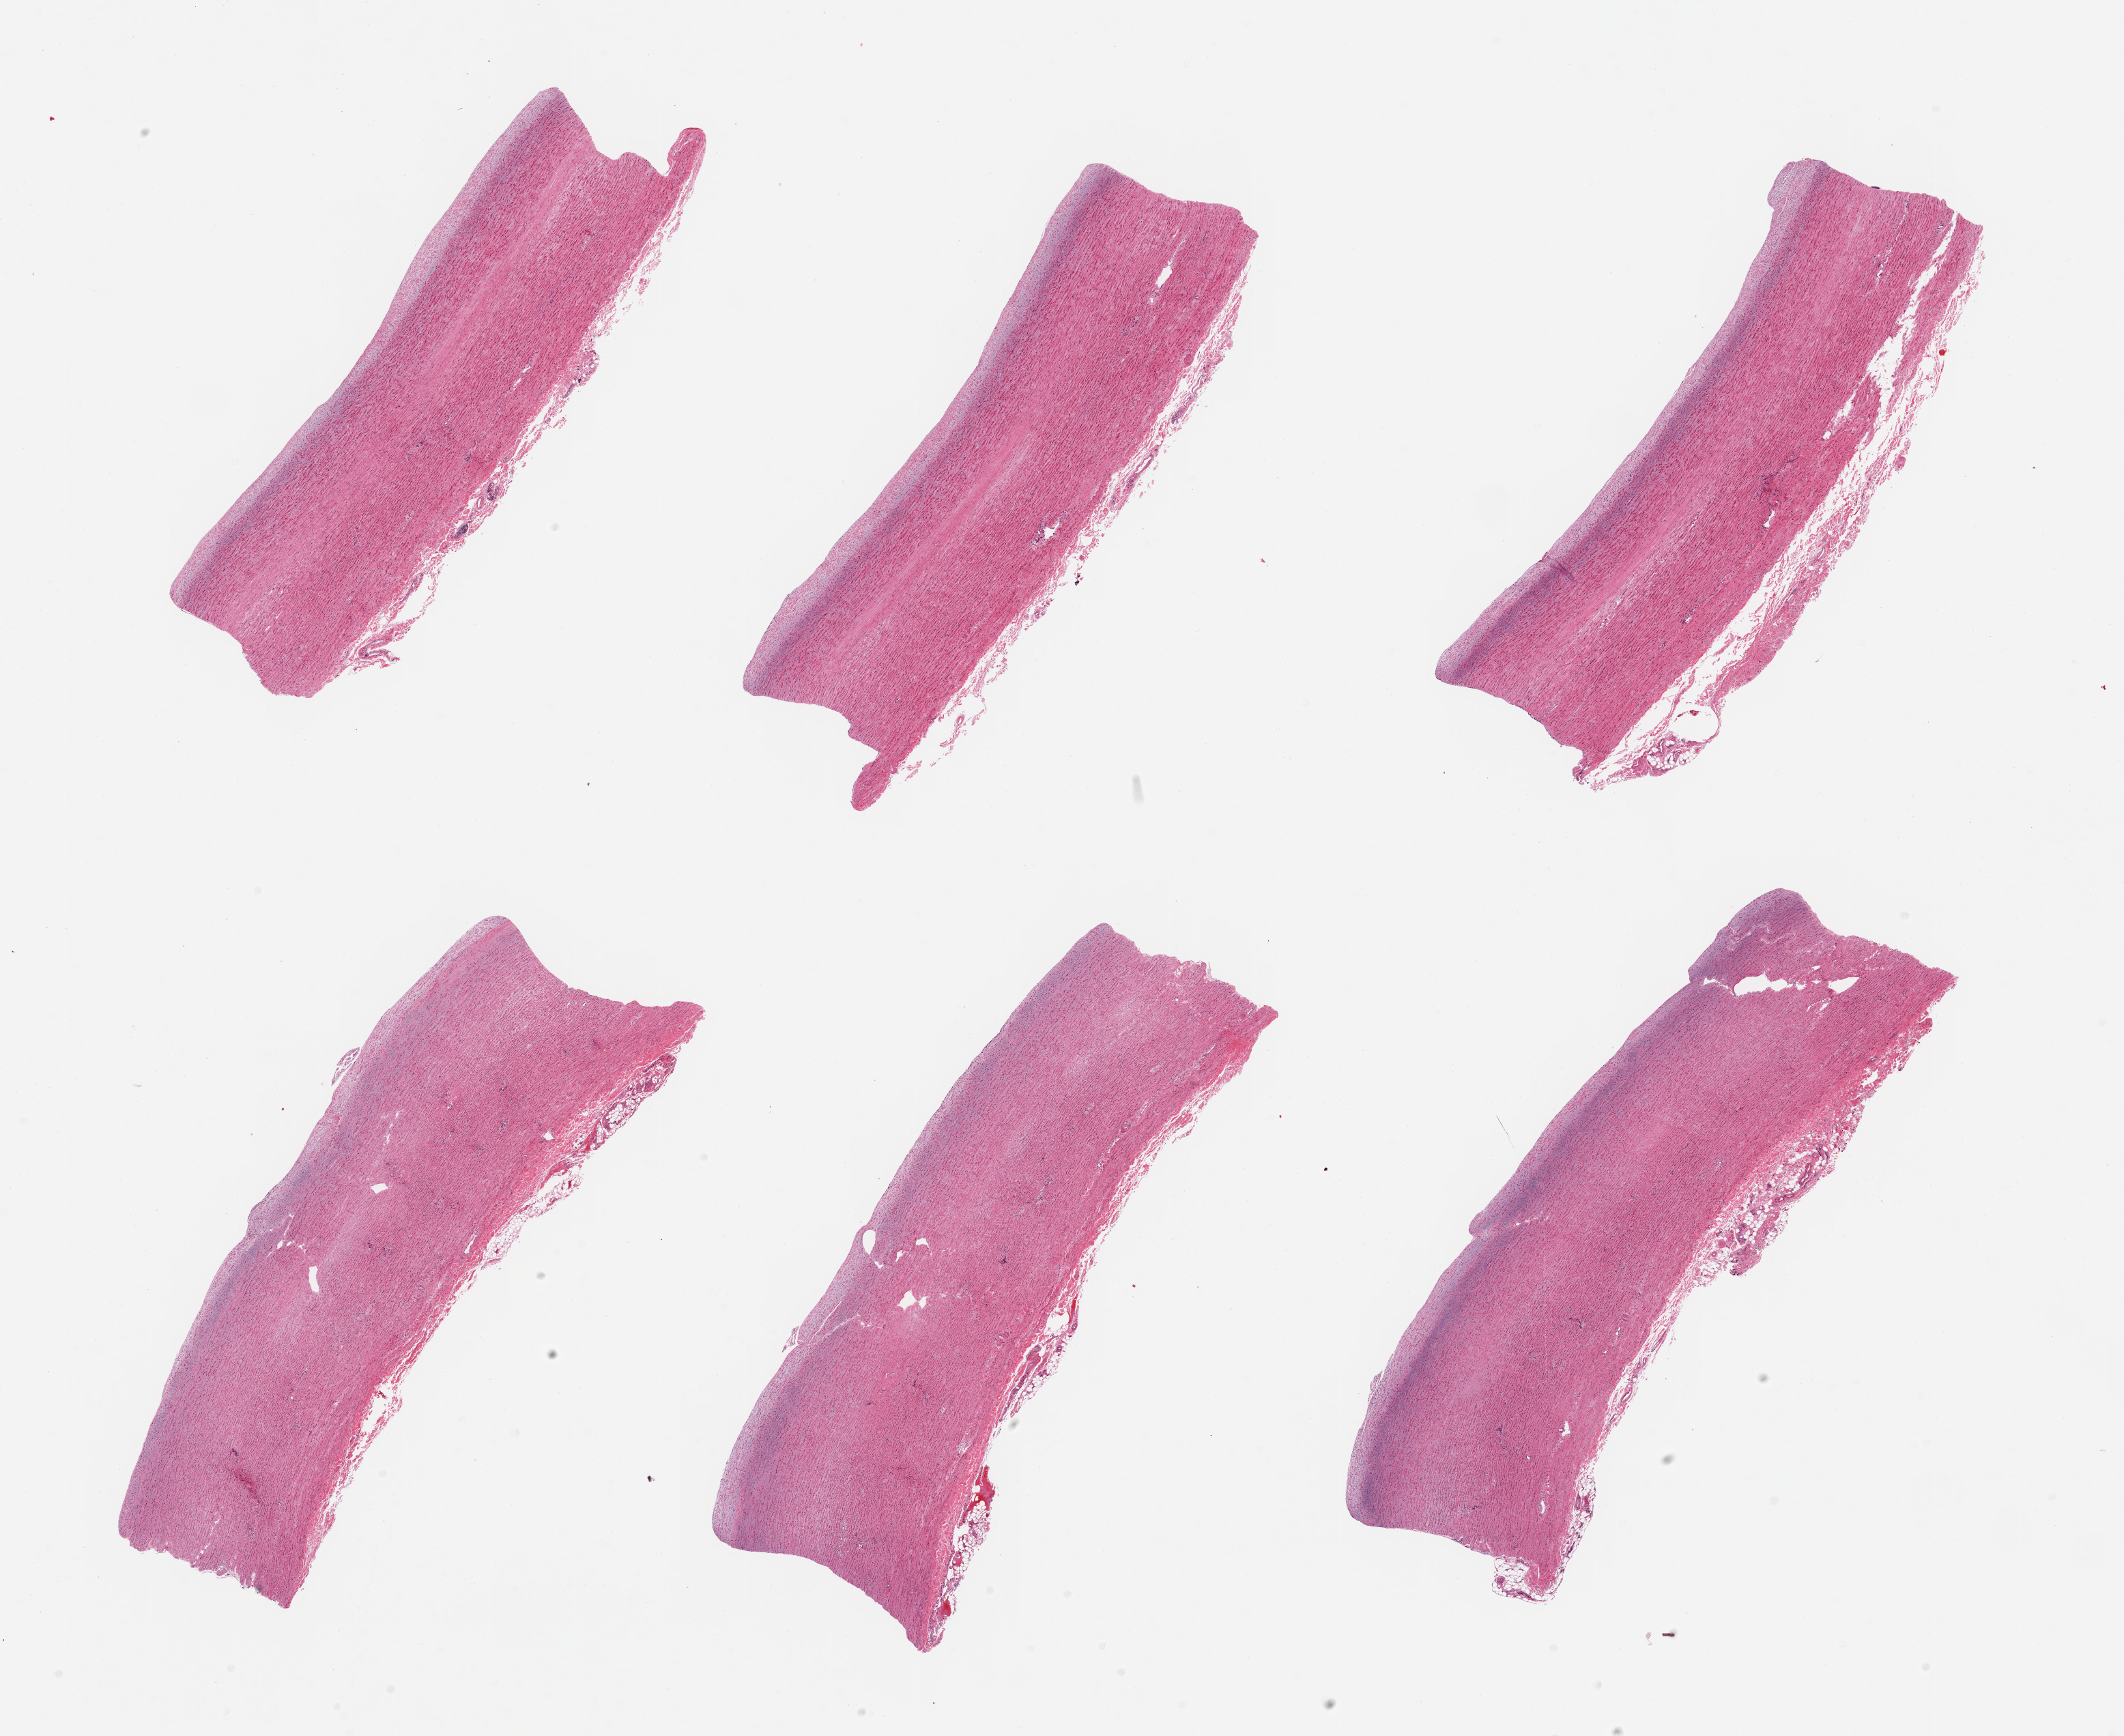
Digitized hematoxylin and eosin (H&E)-stained section, brightfield, shown as a low-resolution overview of the whole scanned area (about 24.6 x 20.1 mm, slide scanned at 20x). PAXgene-fixed paraffin-embedded (PFPE) section. Target tissue: aorta. Tissue donor sample.
* pathologist's review note for this sample: 6 pieces, atherosis up to ~0.3mm